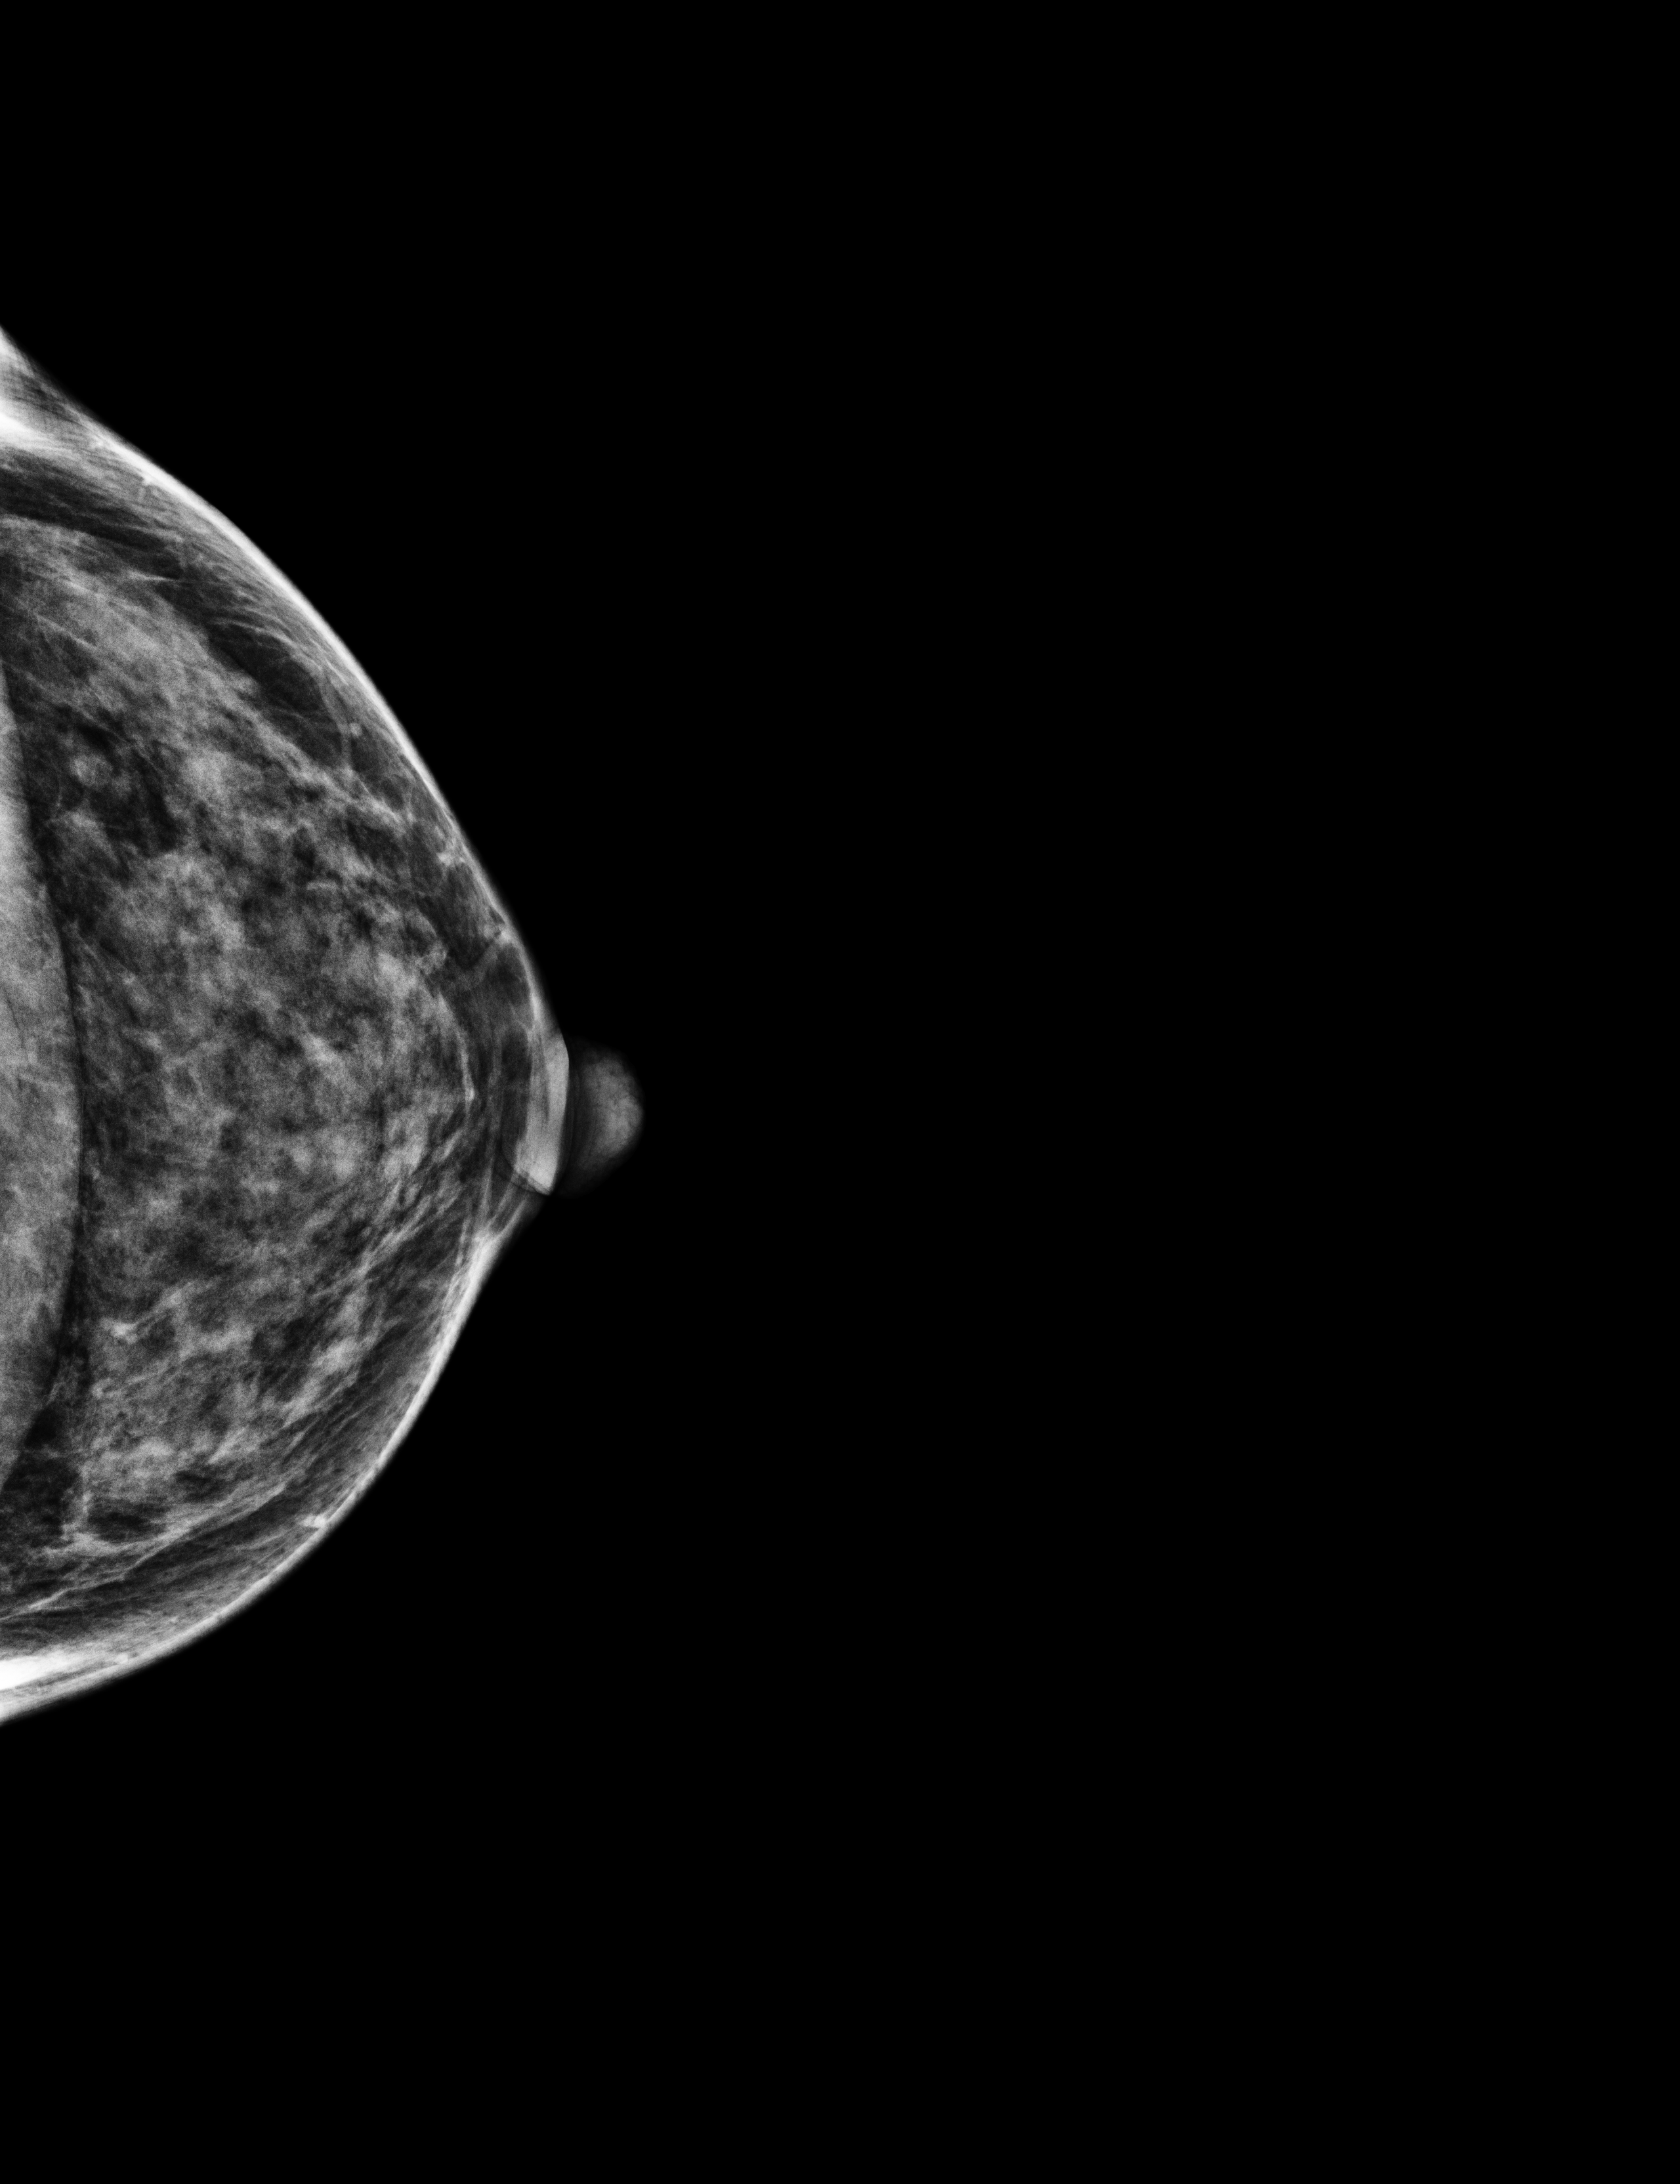
Digital mammogram (FFDM), left breast, CC view, annual screening mammography examination. Patient aged 42 years (female).
BI-RADS breast density category at the screening exam (both breasts, scale 1–4): 3. Final BI-RADS assessment for this screening round (tomosynthesis exam, both breasts): category 1. Recall: no recall after this screen.